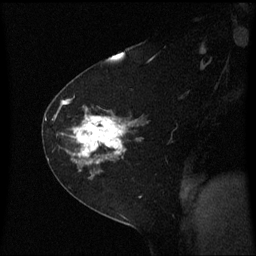
Breast MRI (dynamic contrast-enhanced), one sagittal slice. Dynamic contrast-enhanced series, image 2 of 3 at this slice position (ordered by acquisition). 1.5 T. TE 4.2 ms, TR 8.4 ms. 2 mm slice thickness. 256 × 256 image matrix, field of view 210 × 210 mm. Female patient, age 60 years. Case-level facts recorded for this patient, not image findings: setting: breast cancer imaged before/during neoadjuvant chemotherapy; receptor status: triple-negative.
Structures marked on this image (semi-automatically segmented with operator editing):
- analysis volume of interest (the breast-tissue region the enhancement analysis was run in; not a lesion): box from (x=45, y=99) to (x=146, y=182) px
- tumour enhancement mask (voxels above the 70 % enhancement threshold inside the analysis volume of interest): (x=62, y=100)–(x=127, y=166)